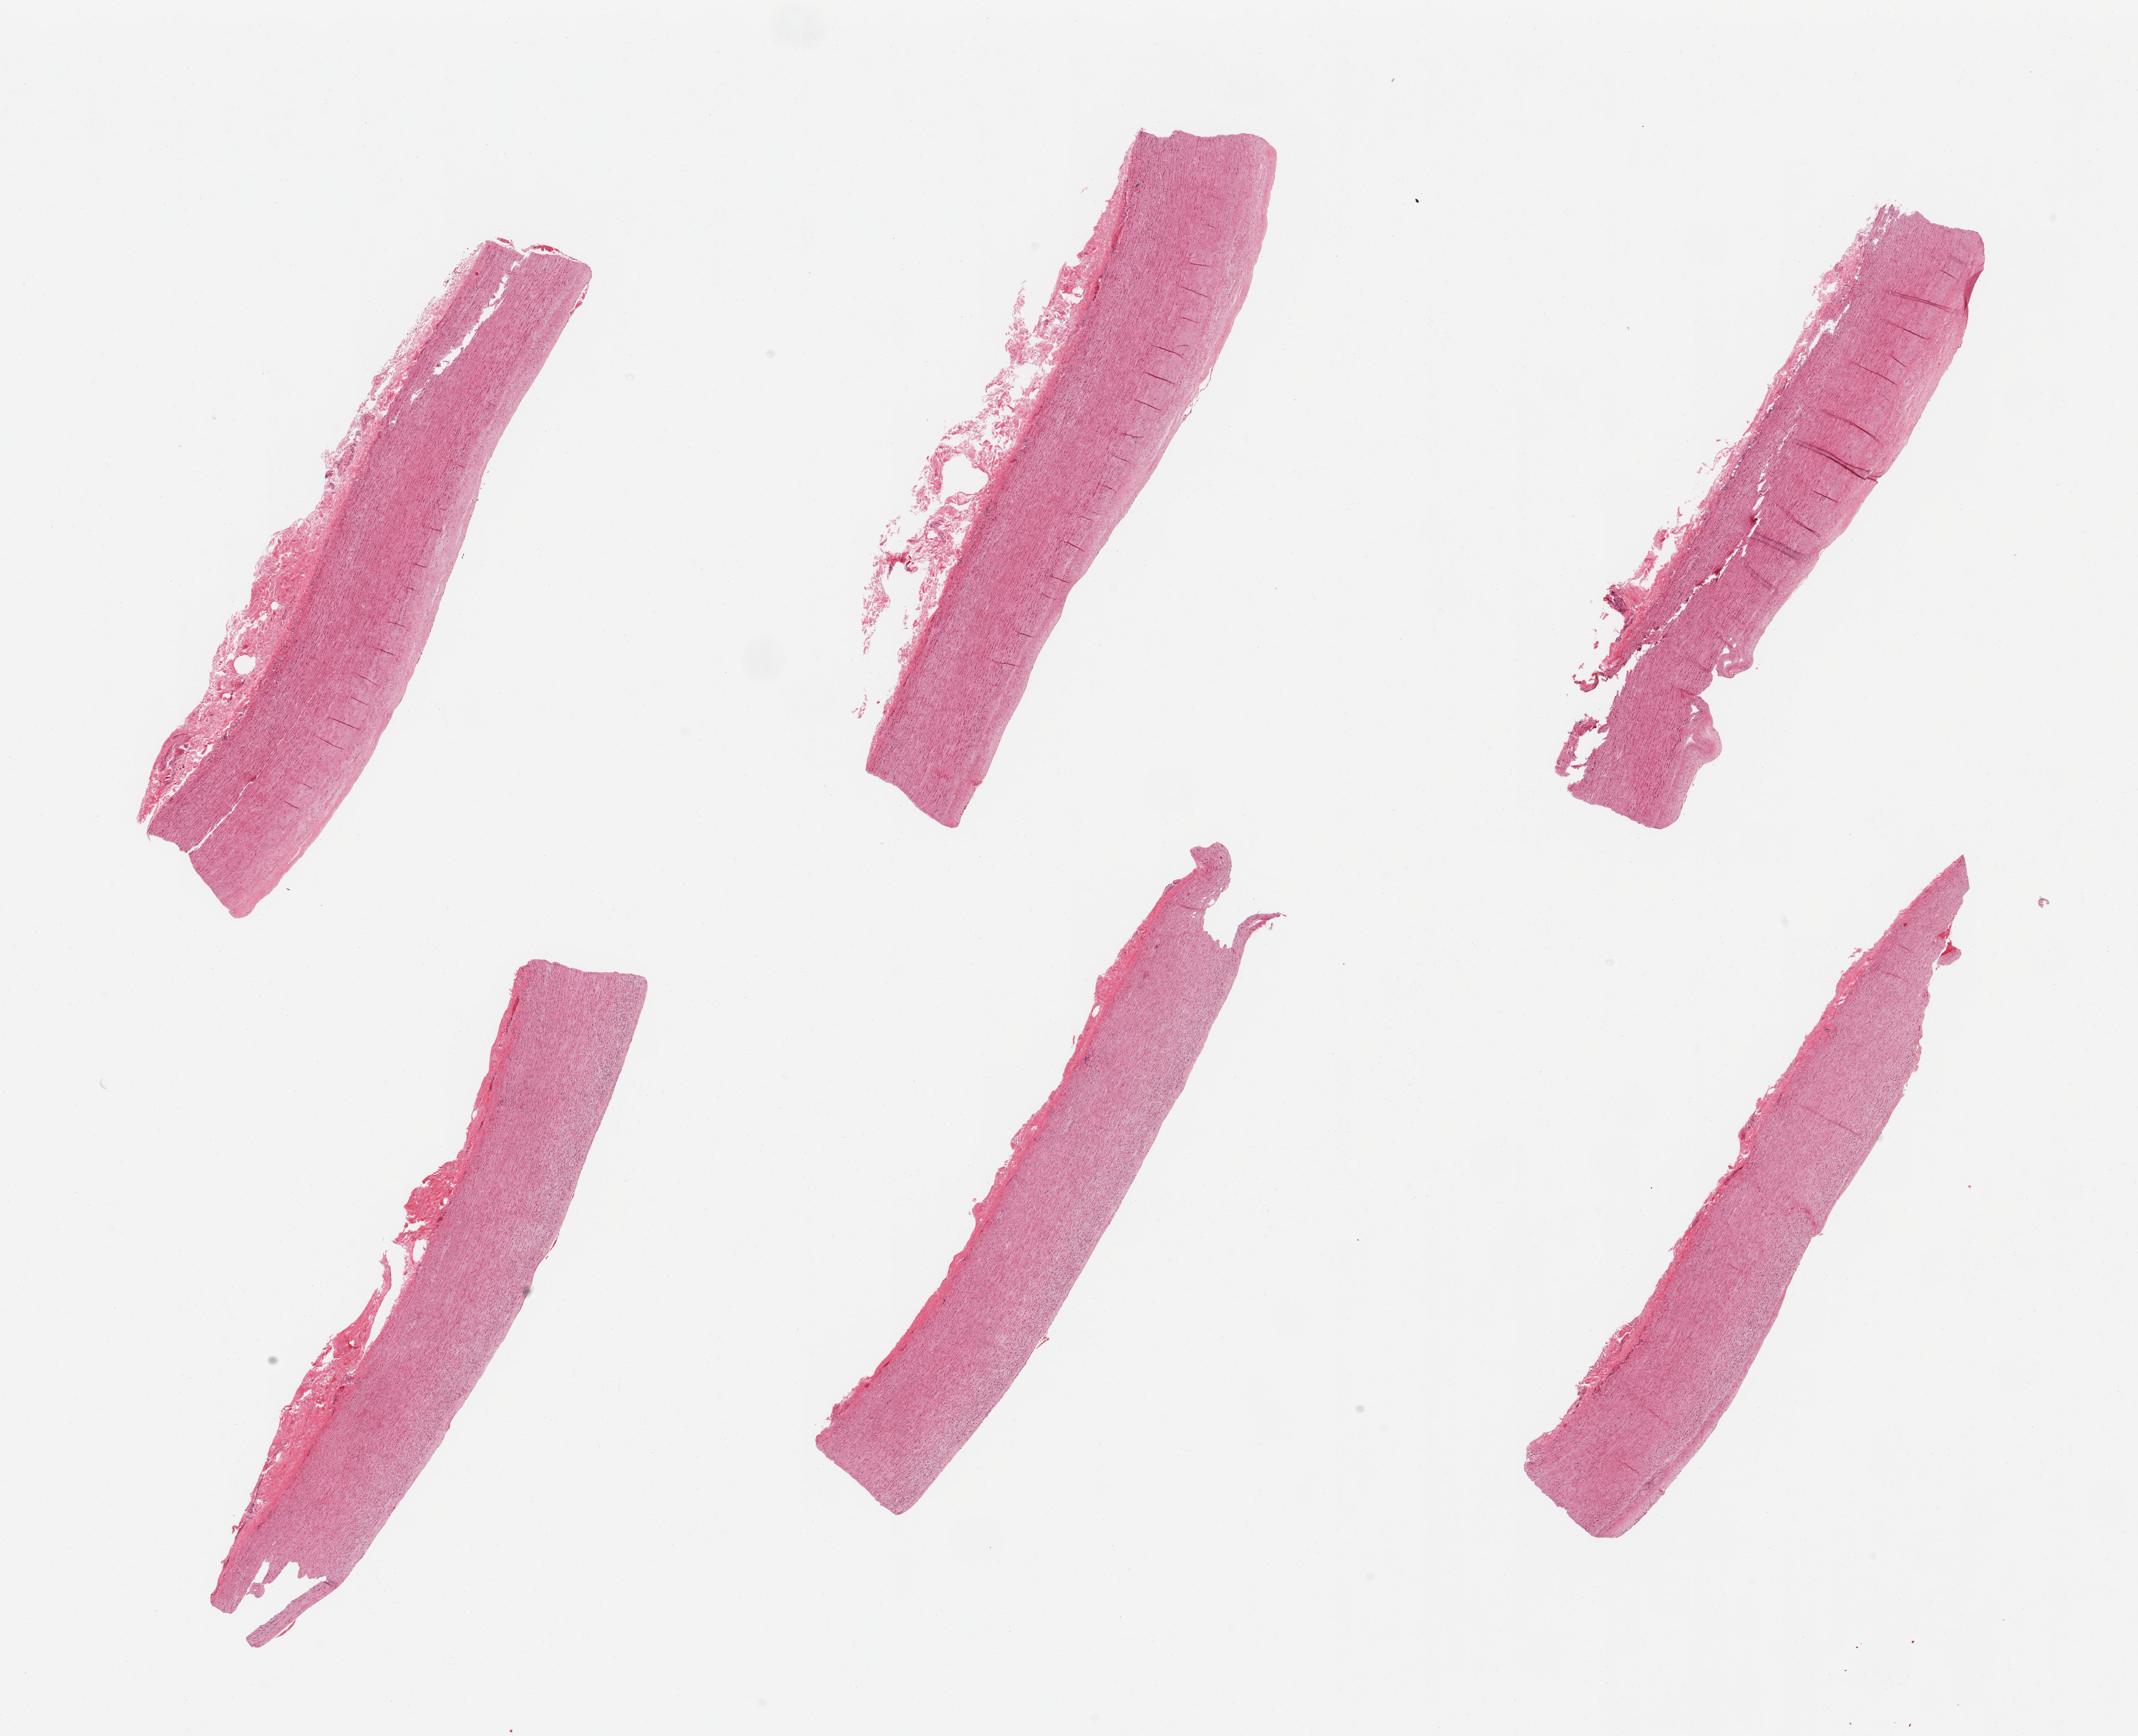
H&E whole-slide image — whole scanned area (about 23.6 x 19.2 mm) shown as a low-resolution overview. PAXgene-fixed, paraffin-embedded tissue. Sampled site (target tissue): aorta. Tissue donor sample. Male donor.
Review note (as recorded): 6 pieces; mild atherosclerosis.